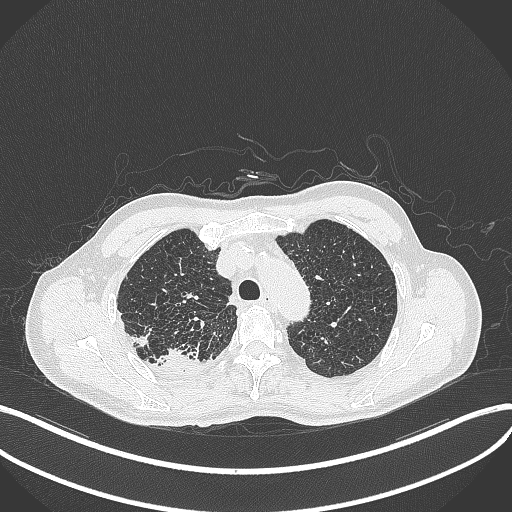
Chest CT, one axial slice; position 348 of 428 along the scan axis; 120 kVp; lung window (W 1500 / L -600 HU); 512 × 512 image matrix. Patient: male, 79 years. From the clinical record (not read from this slice): clinical TNM (as recorded): T3 N0 M0.
Structures marked on this image (bounding box drawn by a radiologist):
- lung tumour (recorded histology: adenocarcinoma): bounding box (x1, y1, x2, y2) in pixels: (159, 346, 202, 375)